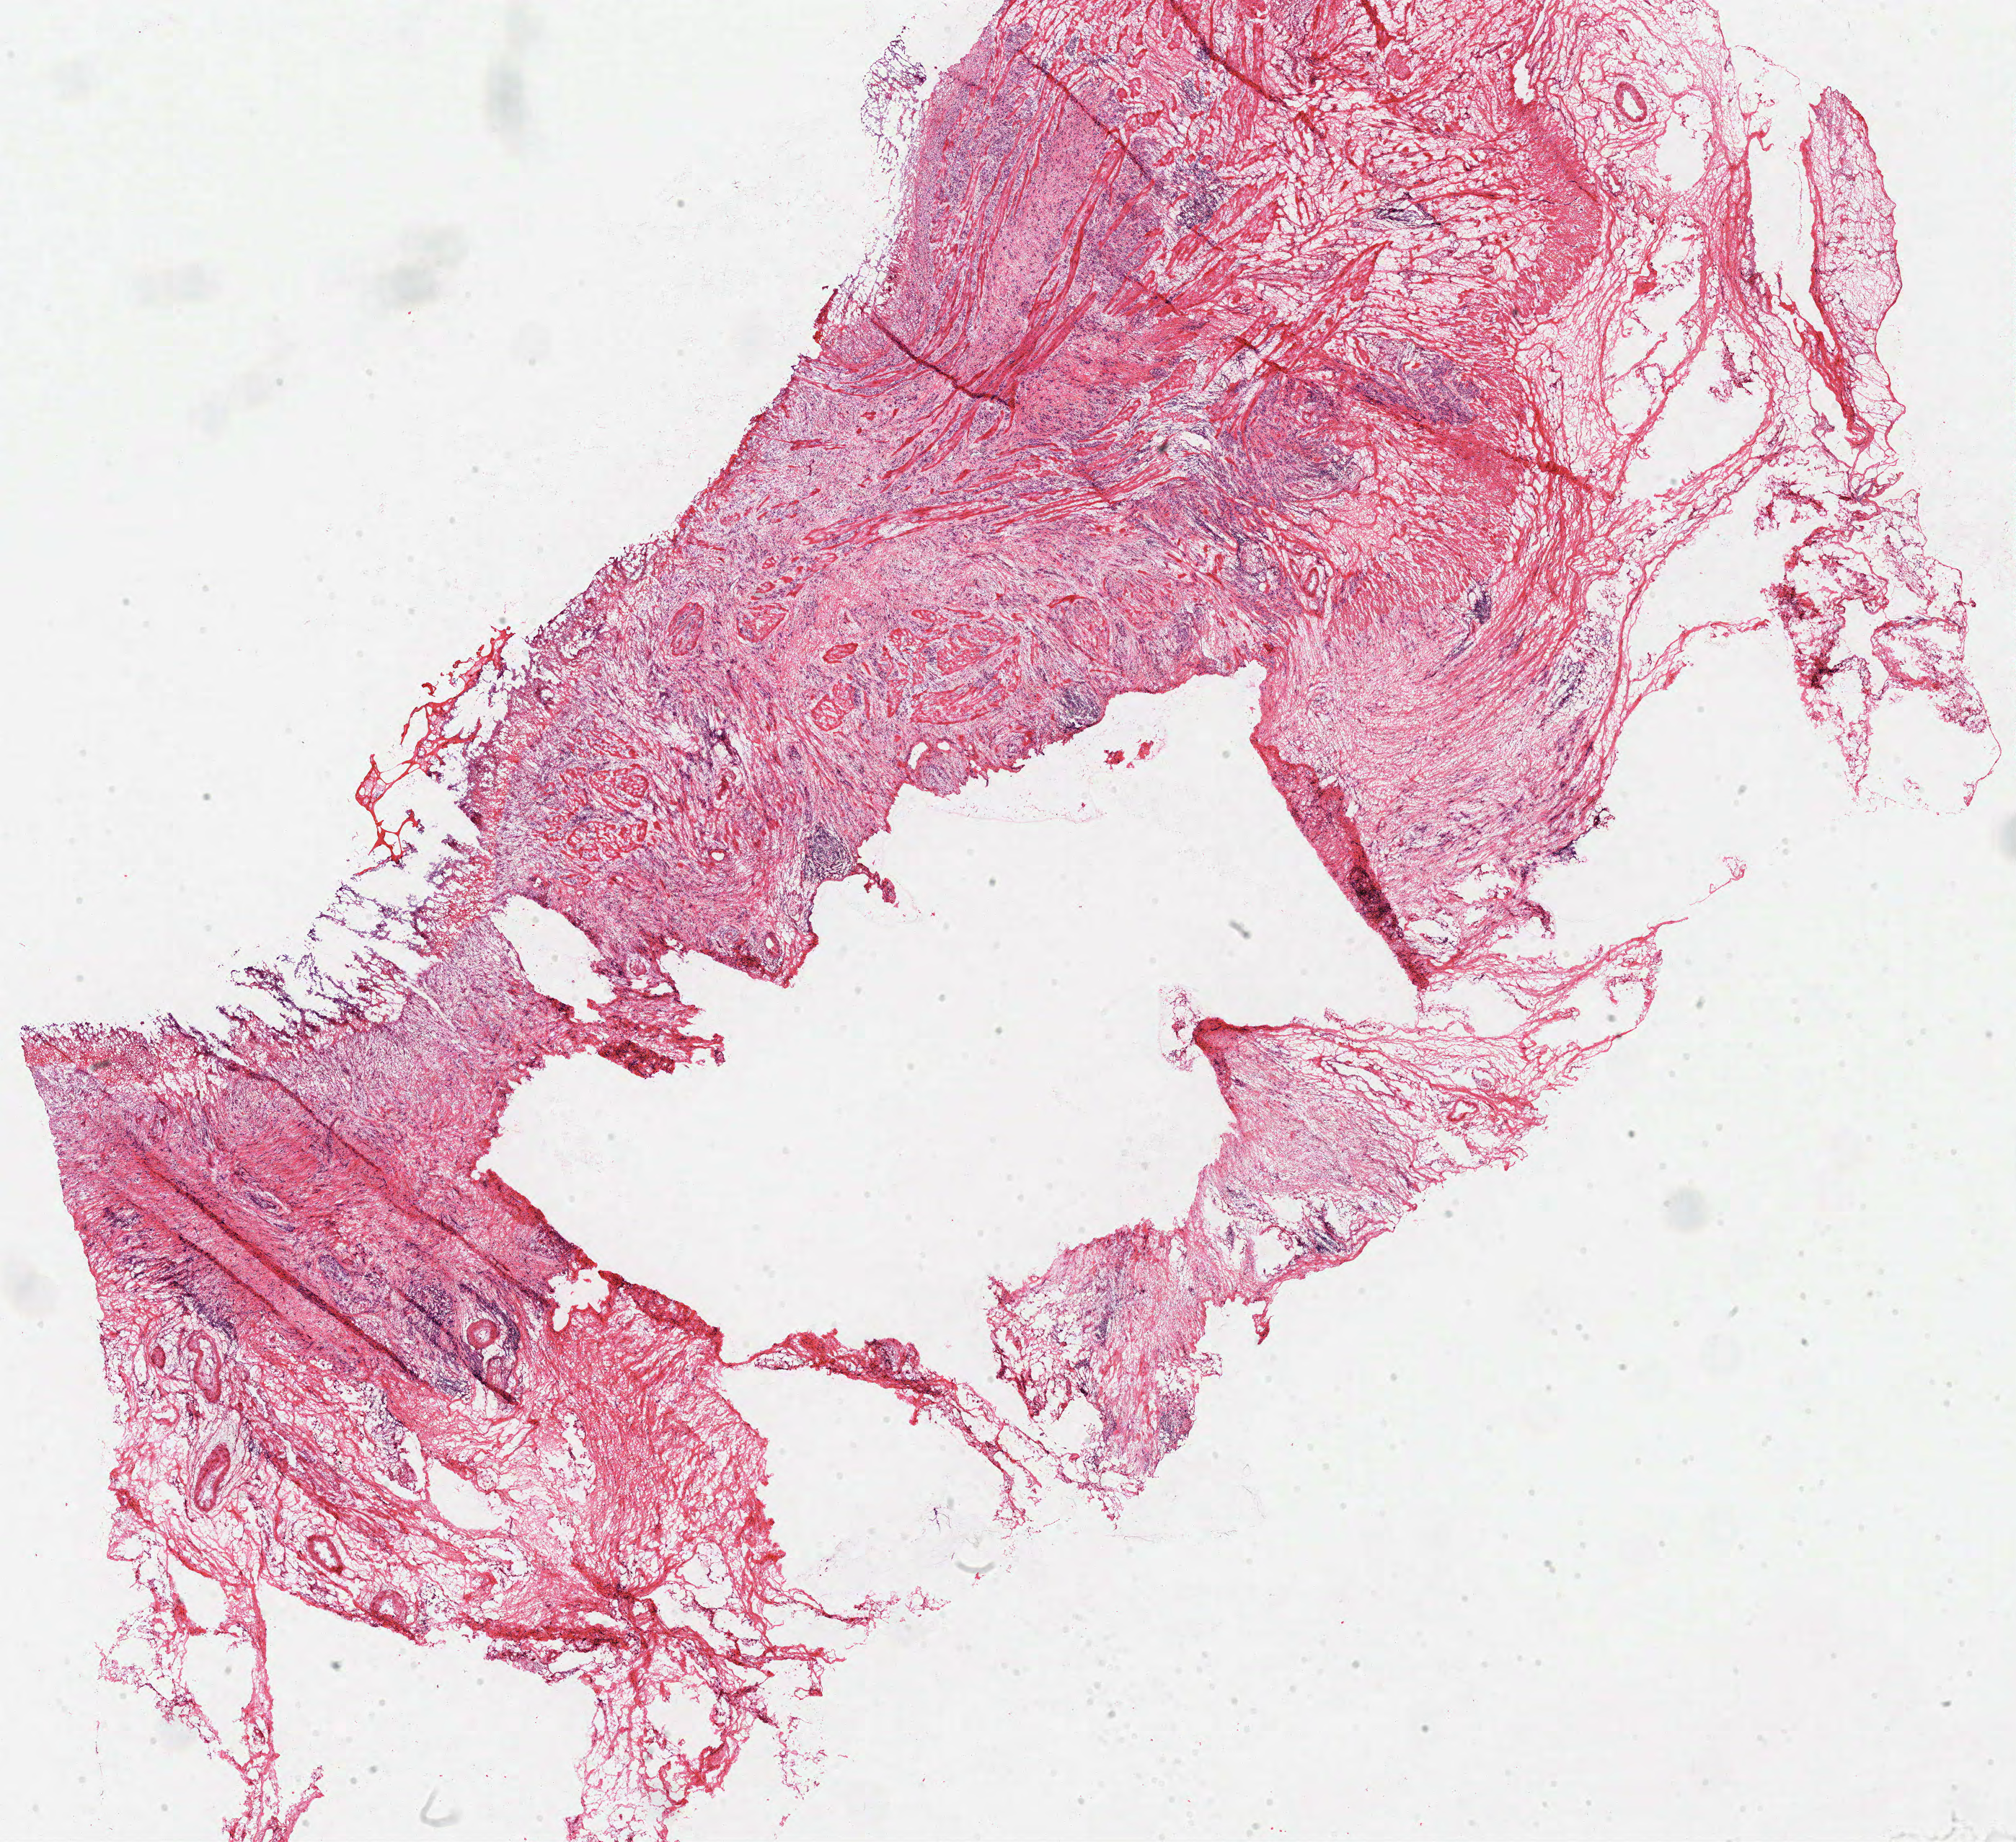
H&E-stained whole-slide image, a low-resolution overview of the entire scanned area, about 22.0 x 20.1 mm, frozen section from the top of the tissue portion, primary tumour sample from the stomach. Female patient; age at initial diagnosis 68 years. Histologic grade: G3 (poorly differentiated). Pathologist review of this section (percent, as recorded): tumour cells 80%, tumour nuclei 70%, normal cells 0%, stromal cells 20%, necrosis 0%.
- AJCC pathologic stage: IIIB
- lymph nodes positive (case pathology): 9 of 12 examined
- diagnosis: Adenocarcinoma, NOS (body of stomach)